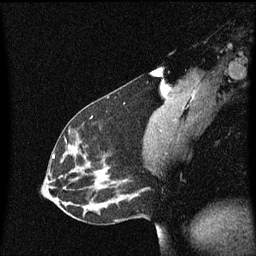
Breast MRI (dynamic contrast-enhanced), one sagittal slice. Slice 29 of 60 in the series (ordered by position). Dynamic contrast-enhanced series, image 2 of 3 at this slice position (ordered by acquisition). 1.5 T. TE 4.2 ms, TR 8.4 ms. 2 mm slice thickness. 256 × 256 image matrix. Female patient, age 33 years.
Structures marked on this image (semi-automatic segmentation, software-assisted and operator-edited):
- analysis volume of interest (the breast-tissue region the enhancement analysis was run in; not a lesion): box from (x=45, y=114) to (x=152, y=191) px
- tumour enhancement mask (voxels above the 70 % enhancement threshold inside the analysis volume of interest): (x=53, y=154)–(x=56, y=159)